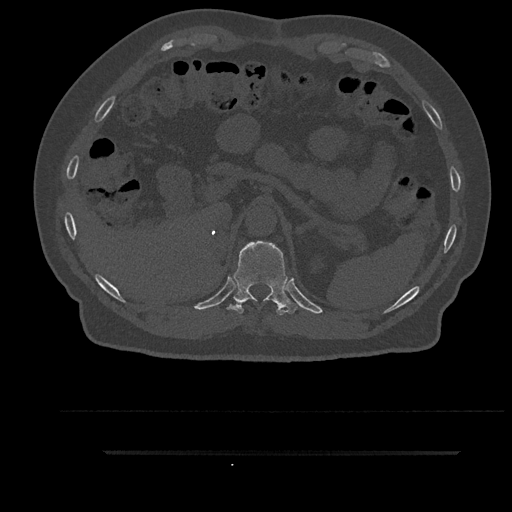
CT including the spine, one axial slice. Slice 318 of 797 in the series (ordered by position). Reconstruction kernel Br40s/3. 120 kVp. Bone window (W 1800 / L 400 HU). 0.5 mm slice thickness. 512 × 512 image matrix, field of view 432 × 432 mm. Patient: male, 63 years. Case-level facts recorded for this patient, not image findings: primary cancer: renal.
Outlined on this slice (semi-automatically segmented with operator editing):
- T11 vertebra: bounding box [x1, y1, x2, y2] px = [227, 241, 297, 315]